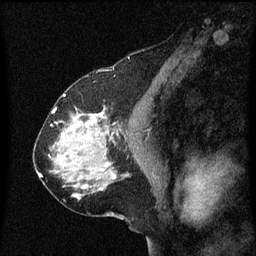
Breast MRI (dynamic contrast-enhanced), one sagittal slice; slice 37 of 60 in the series (ordered by position); dynamic contrast-enhanced series, image 2 of 3 at this slice position (ordered by acquisition); 1.5 T; TE 4.2 ms, TR 8.4 ms; 256 × 256 image matrix, field of view 200 × 200 mm. Patient: female, 58 years.
Annotated regions visible in this slice (semi-automatic segmentation, software-assisted and operator-edited):
- analysis volume of interest (the breast-tissue region the enhancement analysis was run in; not a lesion): box from (x=58, y=114) to (x=99, y=151) px
- tumour enhancement mask (voxels above the 70 % enhancement threshold inside the analysis volume of interest): (x=72, y=114)–(x=99, y=137)